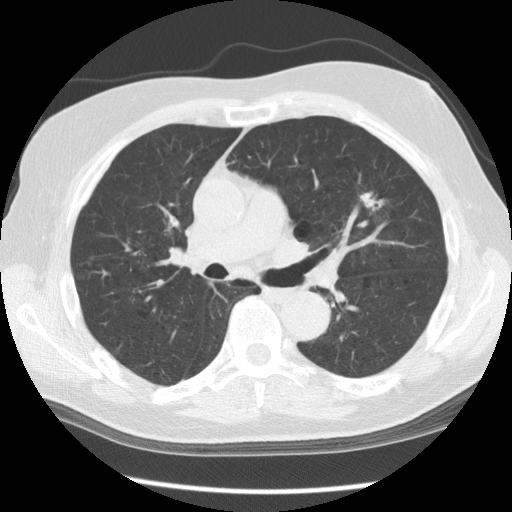
Low-dose screening chest CT, axial slice. Second annual screen. Lung window (W 1500 / L -600 HU). 2.5 mm slice thickness. Male, age 70 years at enrolment. Current smoker at enrolment.
• Expert-annotated lung lesion, bounding box (x1, y1, x2, y2) in pixels: (340, 179, 400, 234).
• The screening reader recorded 3 non-calcified nodules or masses ≥4 mm on this exam (right lower lobe, left upper lobe, left upper lobe); which of them this box marks is not recorded.
• Participant outcome: lung cancer diagnosed 396 days after this screen — adenocarcinoma, NOS, left upper lobe, moderately differentiated (G2), stage IIIA (AJCC 6th edition), 17 mm at pathology.